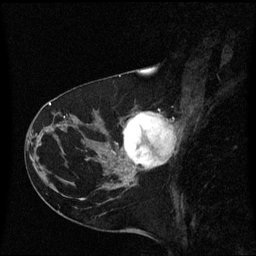
Breast MRI (dynamic contrast-enhanced), one sagittal slice; slice 26 of 60 in the series (ordered by position); dynamic contrast-enhanced series, image 2 of 3 at this slice position (ordered by acquisition); 1.5 T; TE 4.2 ms, TR 8.4 ms; 2 mm slice thickness; 256 × 256 image matrix, field of view 220 × 220 mm. Patient: female, 41 years. Case-level facts recorded for this patient, not image findings: setting: breast cancer imaged before/during neoadjuvant chemotherapy; receptor status: triple-negative.
Structures marked on this image (semi-automatic segmentation, software-assisted and operator-edited):
- analysis volume of interest (the breast-tissue region the enhancement analysis was run in; not a lesion): bounding box [x1, y1, x2, y2] px = [116, 108, 179, 177]
- tumour enhancement mask (voxels above the 70 % enhancement threshold inside the analysis volume of interest): [123, 112, 173, 169]